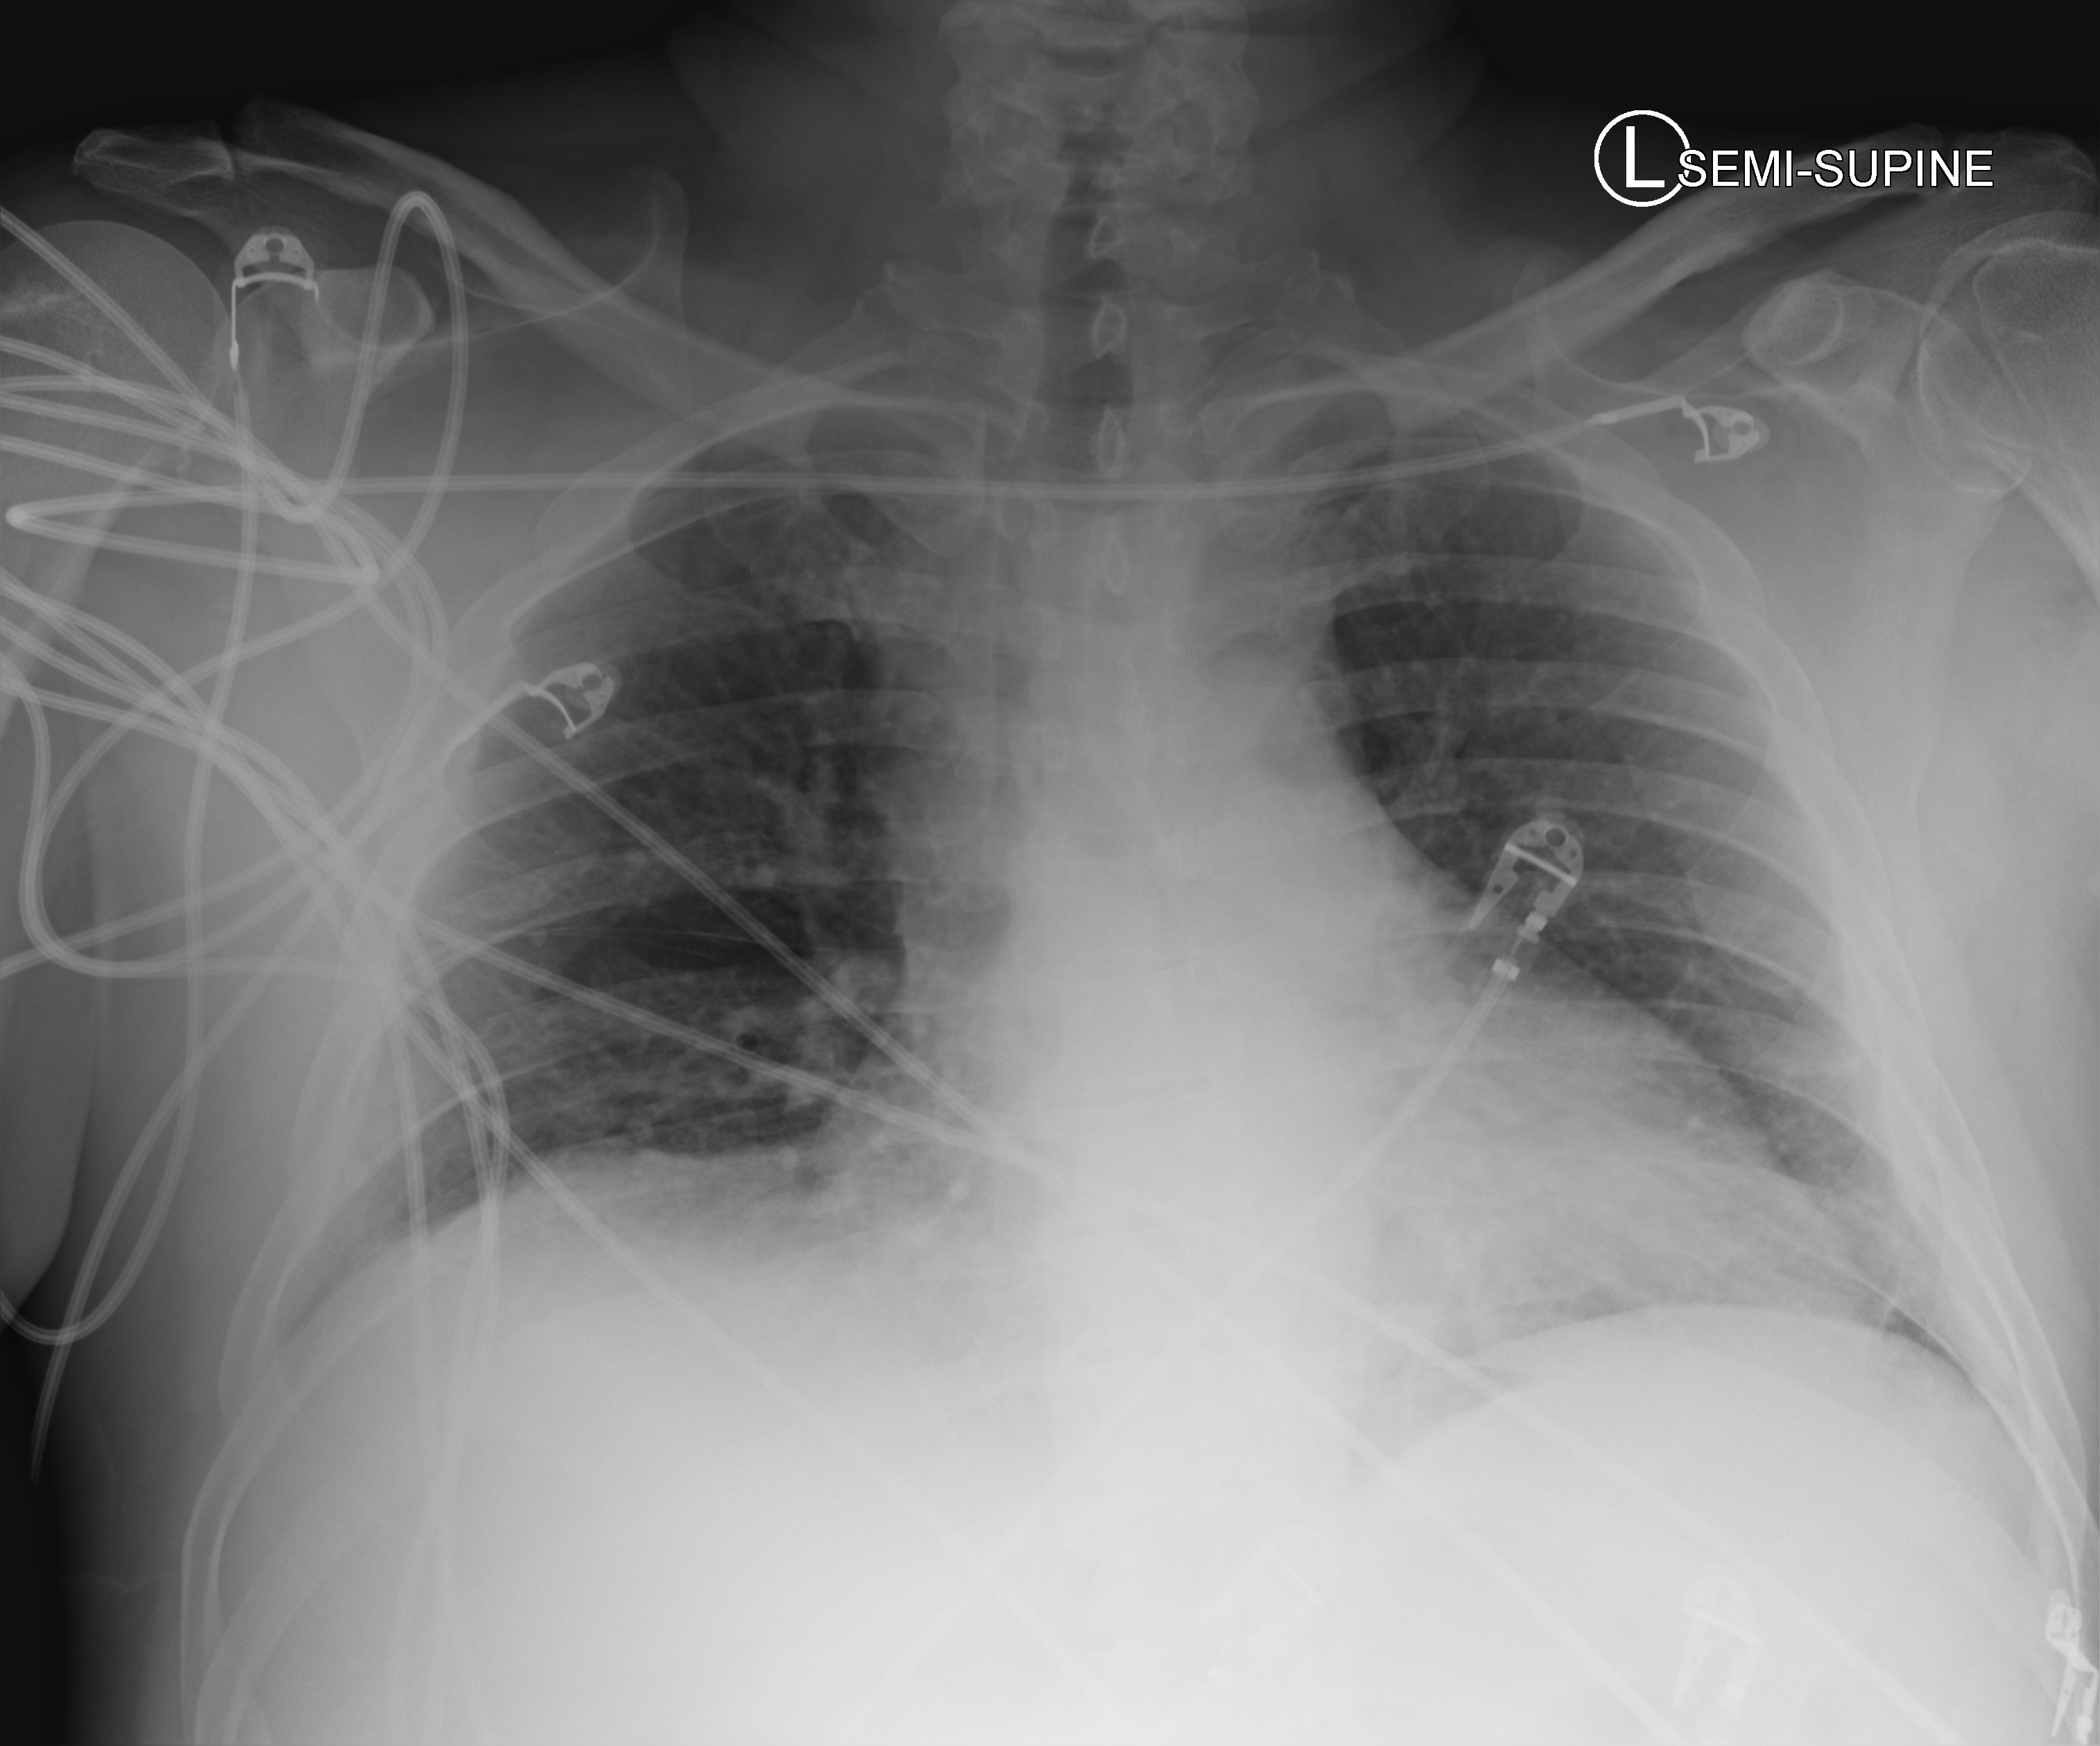
Chest X-ray (portable), anteroposterior (AP) projection. Patient hospitalised with COVID-19; male, aged 18–59 years.
Admission-level facts for this patient (not findings on this image; timing relative to this image not recorded): COPD (admission record): no; mechanically ventilated during this hospital stay: yes.